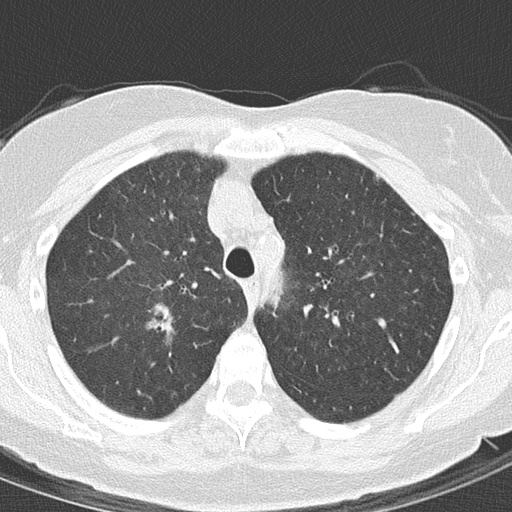
Low-dose screening chest CT, axial slice; second annual screen; lung window (W 1500 / L -600 HU); 120 kVp. Female, age 61 years at enrolment. Current smoker at enrolment.
Expert-annotated lung lesion, bounding box (x1, y1, x2, y2) in pixels: (146, 305, 188, 342). Reader record for this screening exam (exam-level; its link to the box is not recorded): non-calcified nodule or mass ≥4 mm, right upper lobe, 15 × 10 mm, spiculated (stellate) margins, ground glass attenuation, pre-existing on the prior screen: yes; interval growth: yes. Later outcome: lung cancer diagnosed 91 days after this screen — adenocarcinoma, NOS, right upper lobe, moderately differentiated (G2), stage IA (AJCC 6th edition), 20 mm at pathology.